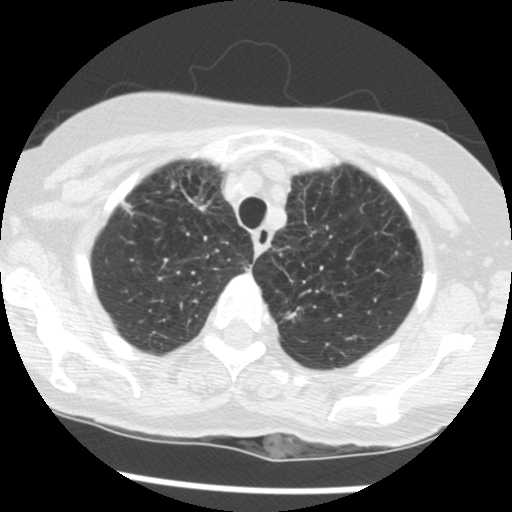
Low-dose screening chest CT, axial slice; second annual screen; lung window (W 1500 / L -600 HU); standard (soft-tissue) reconstruction kernel (STANDARD); slice 22 of 124 in the series; 512 × 512 image matrix, field of view 290 × 290 mm. Female participant, aged 70 years at enrolment.
Lesion marked by an expert reader, bounding box [x1, y1, x2, y2] px = [158, 180, 222, 235]. The exam's reader record, not a measurement of the box and not confirmed to be the same lesion: non-calcified nodule or mass ≥4 mm, right upper lobe, 11 × 7 mm, spiculated (stellate) margins, soft tissue attenuation, pre-existing on the prior screen: yes; interval growth: yes. Official screen result: positive, other. Later outcome: lung cancer diagnosed 248 days after this screen — non-small cell carcinoma, right upper lobe, stage IV (AJCC 6th edition), 30 mm at pathology.